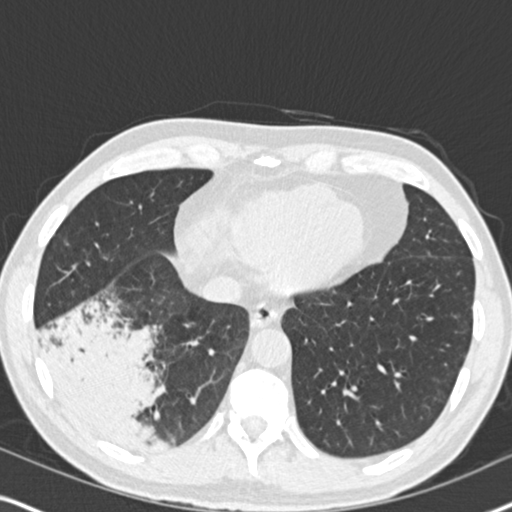
Low-dose screening chest CT, one axial slice. Position 62 of 182 along the scan axis. Lung window (W 1500 / L -600 HU). 2 mm slice thickness. 512 × 512 image matrix, field of view 330 × 330 mm.
Annotated regions visible in this slice (expert manual segmentation):
- lesion 1 (tumor, lower lobe of right lung): bounding box [x1, y1, x2, y2] px = [45, 324, 156, 449]